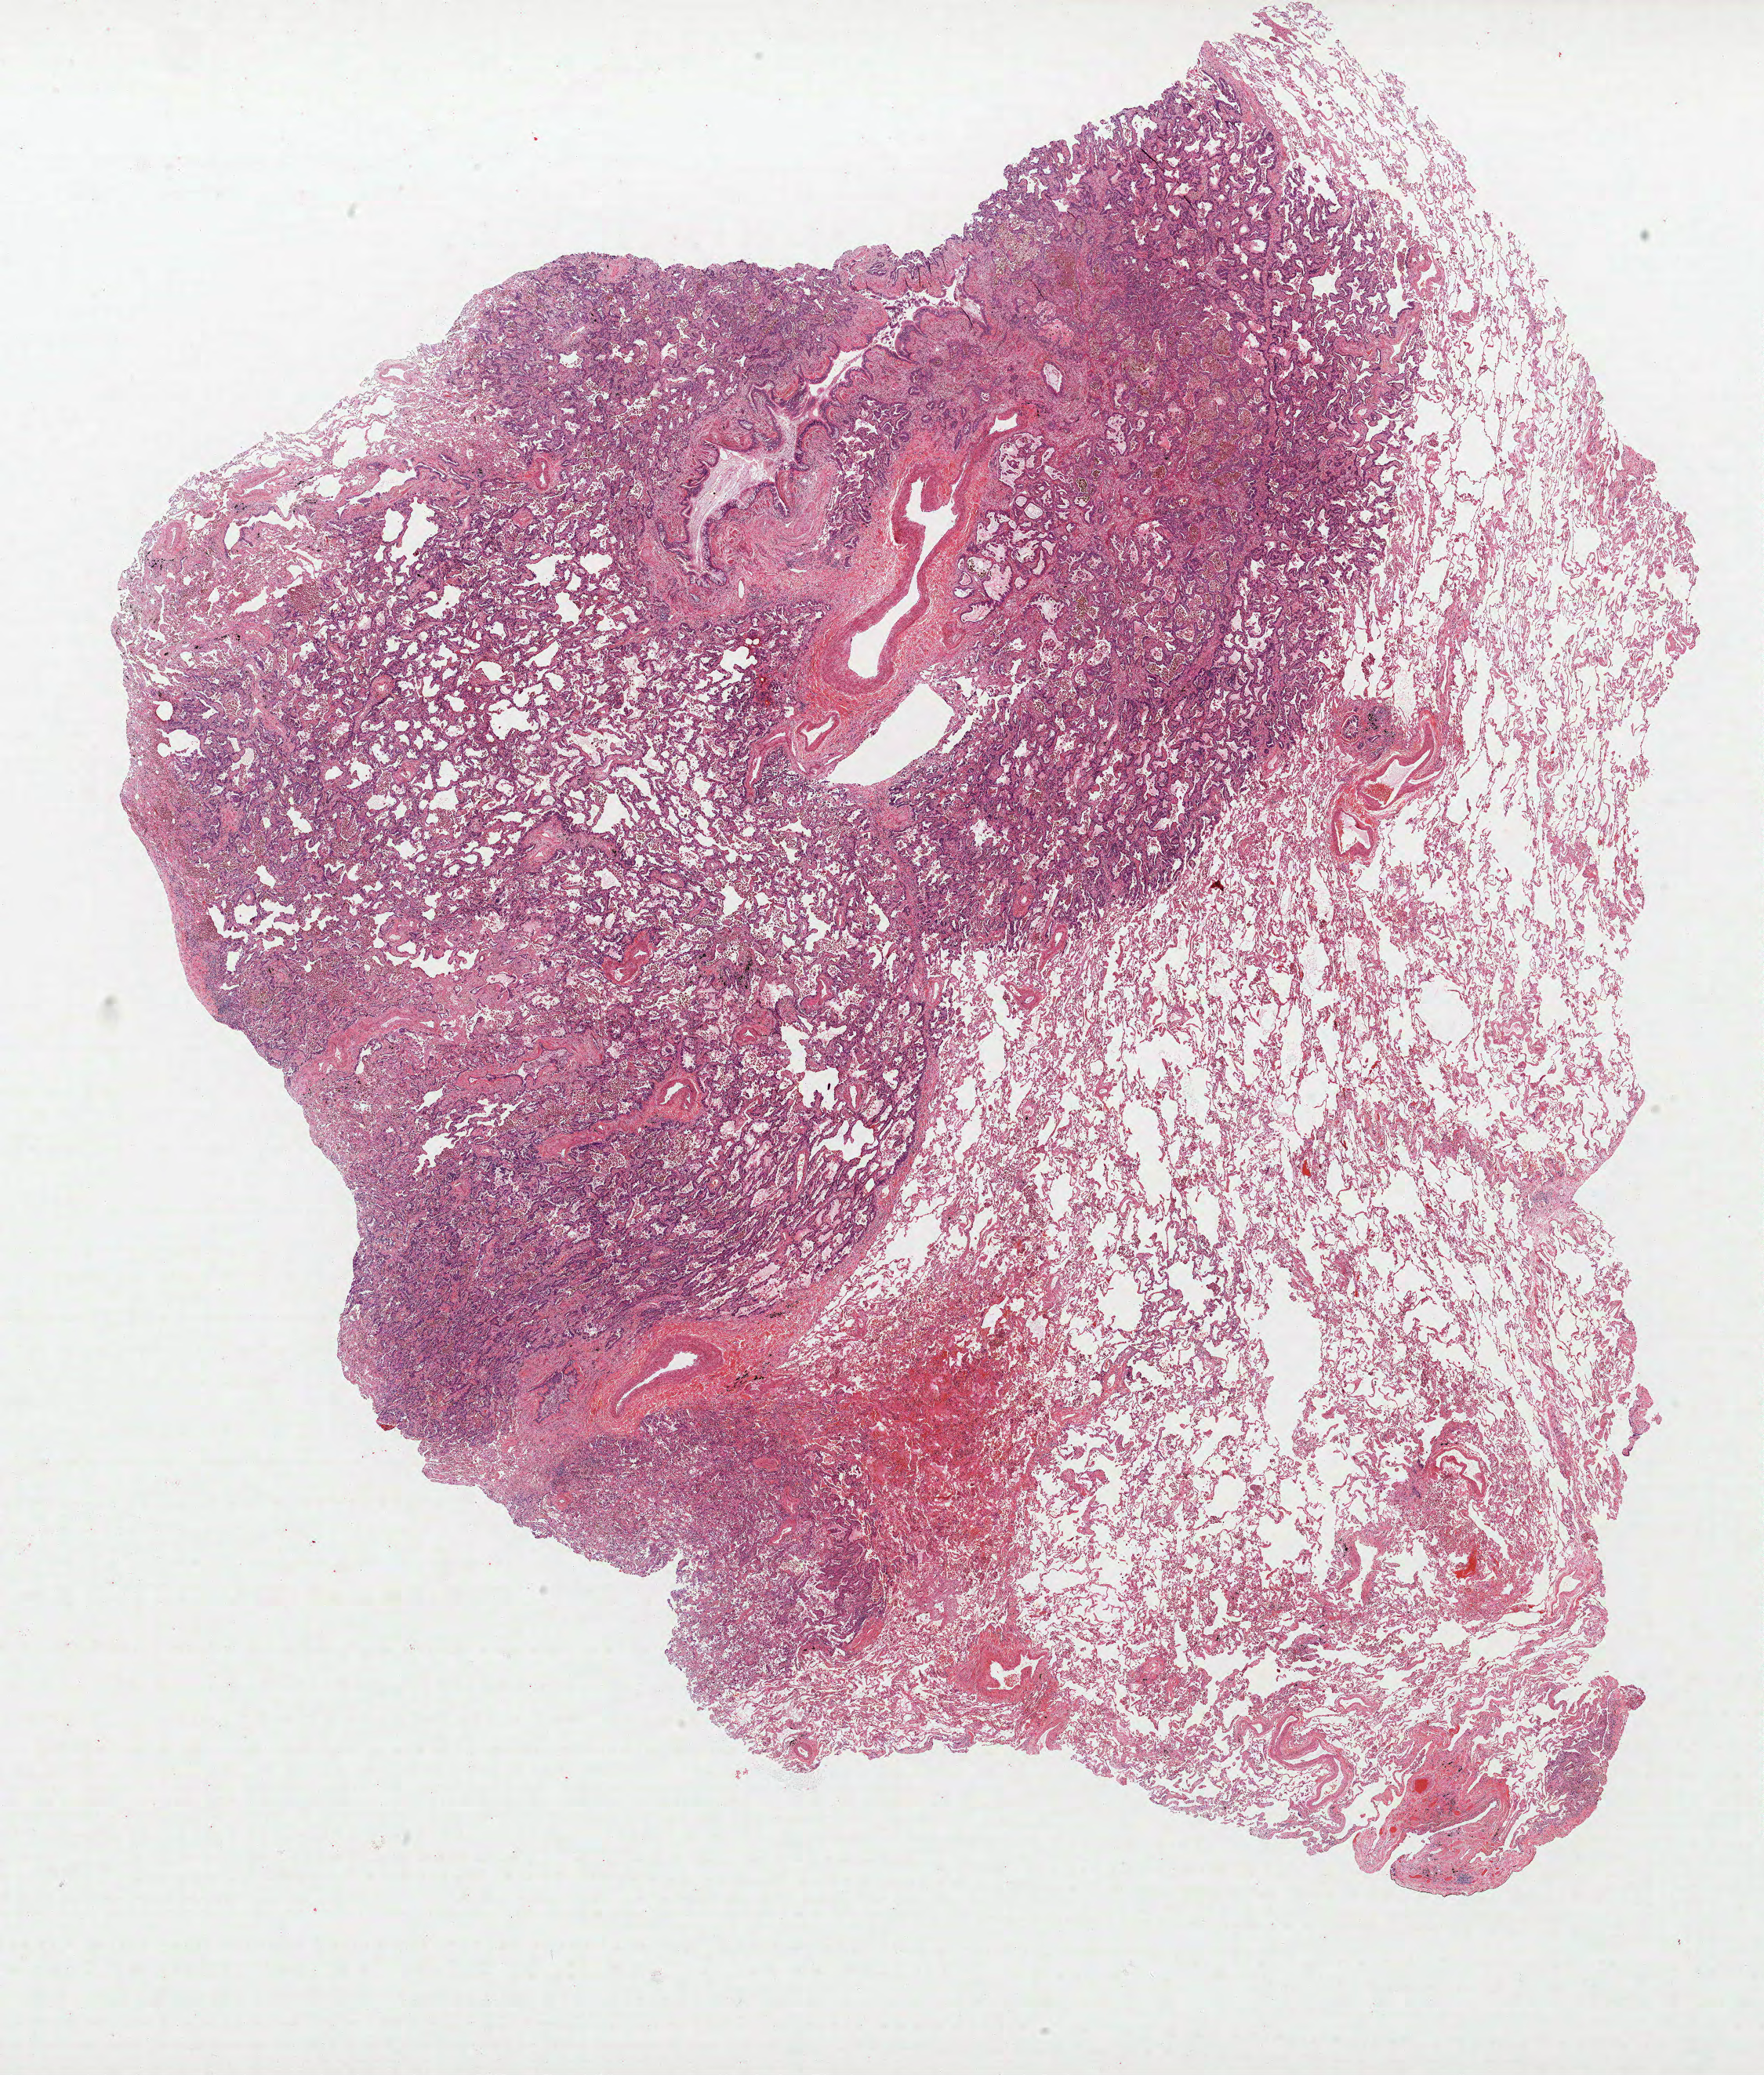
Hematoxylin and eosin (H&E) stained whole-slide image, low-resolution overview of the scanned area, about 18.0 x 21.2 mm, formalin-fixed paraffin-embedded (FFPE) section, lung tissue. Male patient, aged 57 at enrolment. Current smoker at enrolment. Grade: well differentiated (G1).
Tumour size (pathology): 30 mm. Participant's lung-cancer diagnosis: Adenocarcinoma, NOS. ICD-O-3 topography: upper lobe of lung (C34.1). Primary tumour location (clinical record): left upper lobe. Stage (AJCC 6th edition): IA.